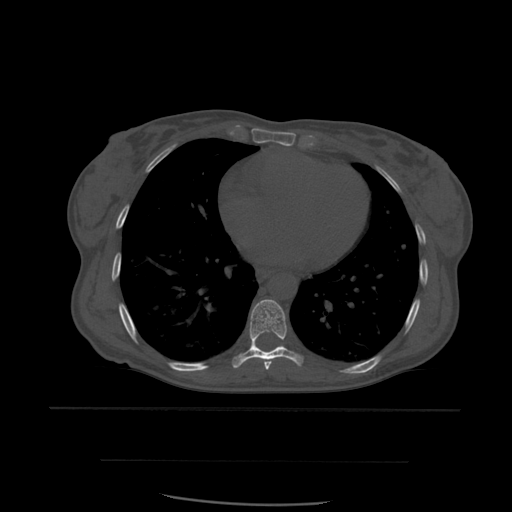
CT including the spine, one axial slice; position 357 of 574 along the scan axis; bone window (W 1800 / L 400 HU); 1.25 mm slice thickness; 512 × 512 image matrix. Patient age 48 years. From the clinical record (not read from this slice): primary cancer: lung; vertebrae with lytic lesions (as recorded): T11.
Annotated regions visible in this slice (semi-automatically segmented with operator editing):
- T7 vertebra: box from (x=264, y=362) to (x=272, y=370) px
- T8 vertebra: (x=232, y=299)–(x=304, y=369)